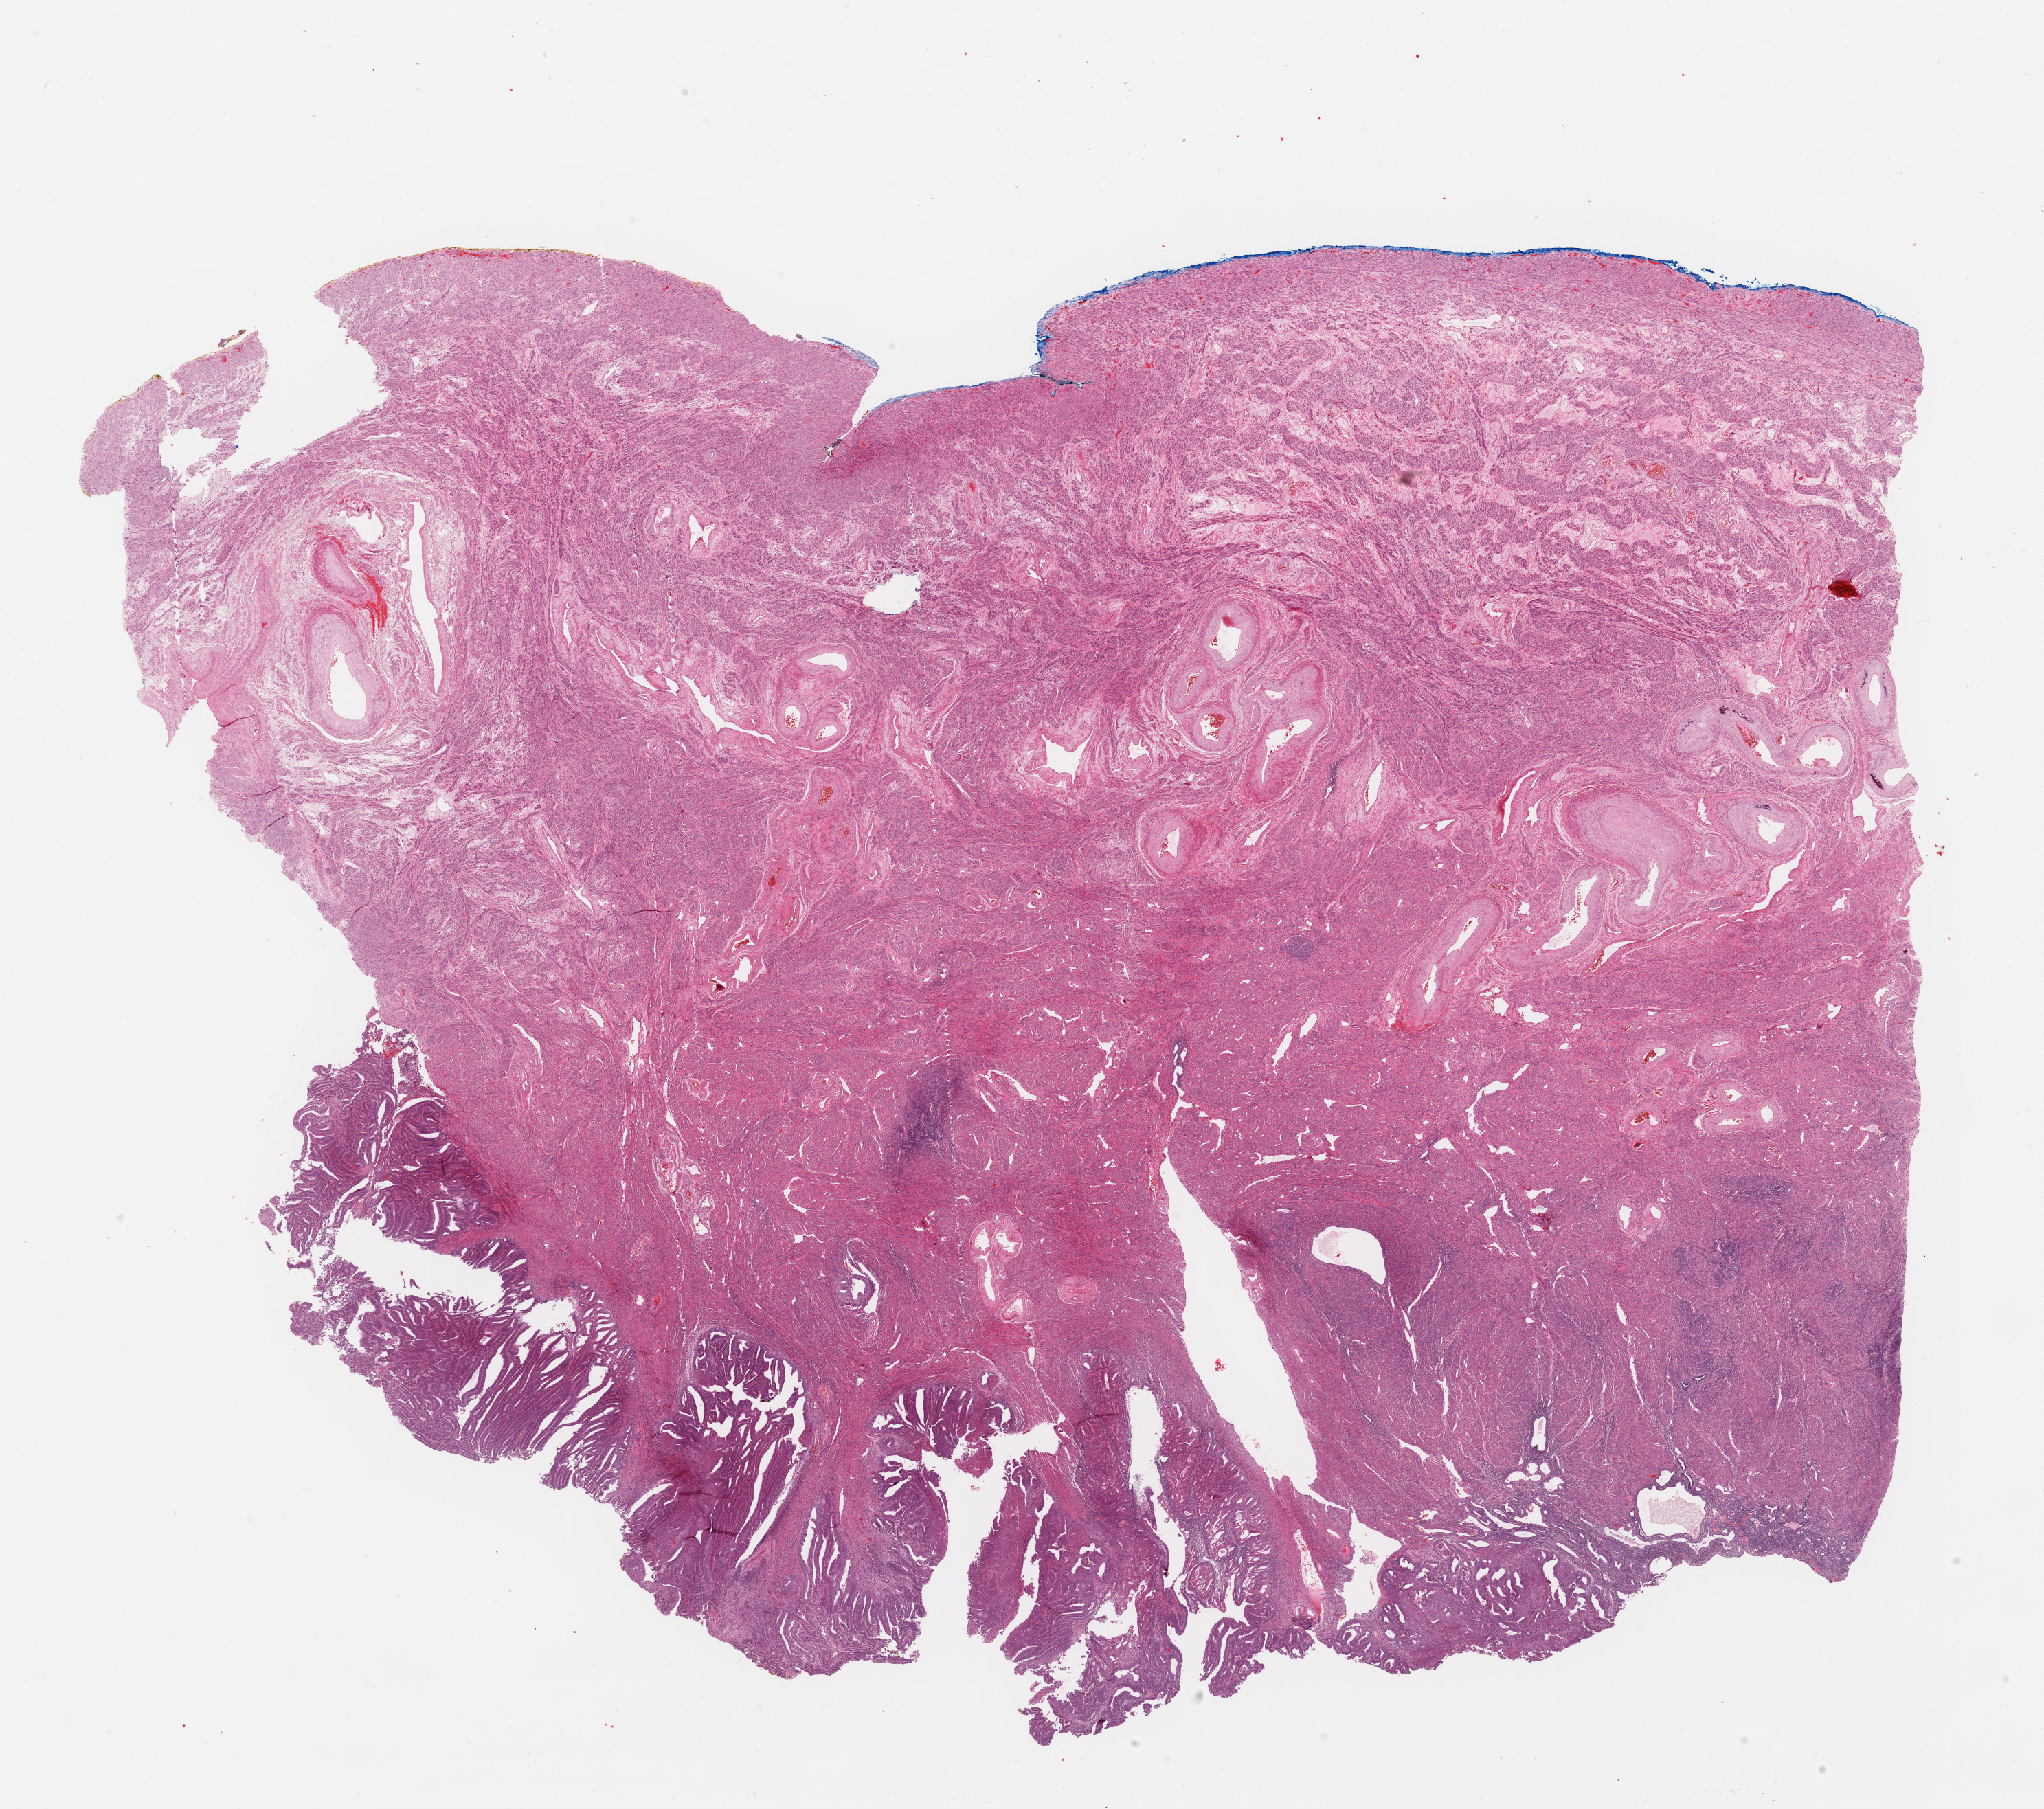
Digitized H&E-stained tissue section (whole slide) — low-resolution overview of the scanned area, about 23.5 x 20.8 mm; FFPE section; uterus, primary tumour sample. Female, age 82 years at initial diagnosis. Histologic grade: G1 (well differentiated).
Diagnosis: Endometrioid adenocarcinoma, NOS (endometrium). FIGO stage: IB.